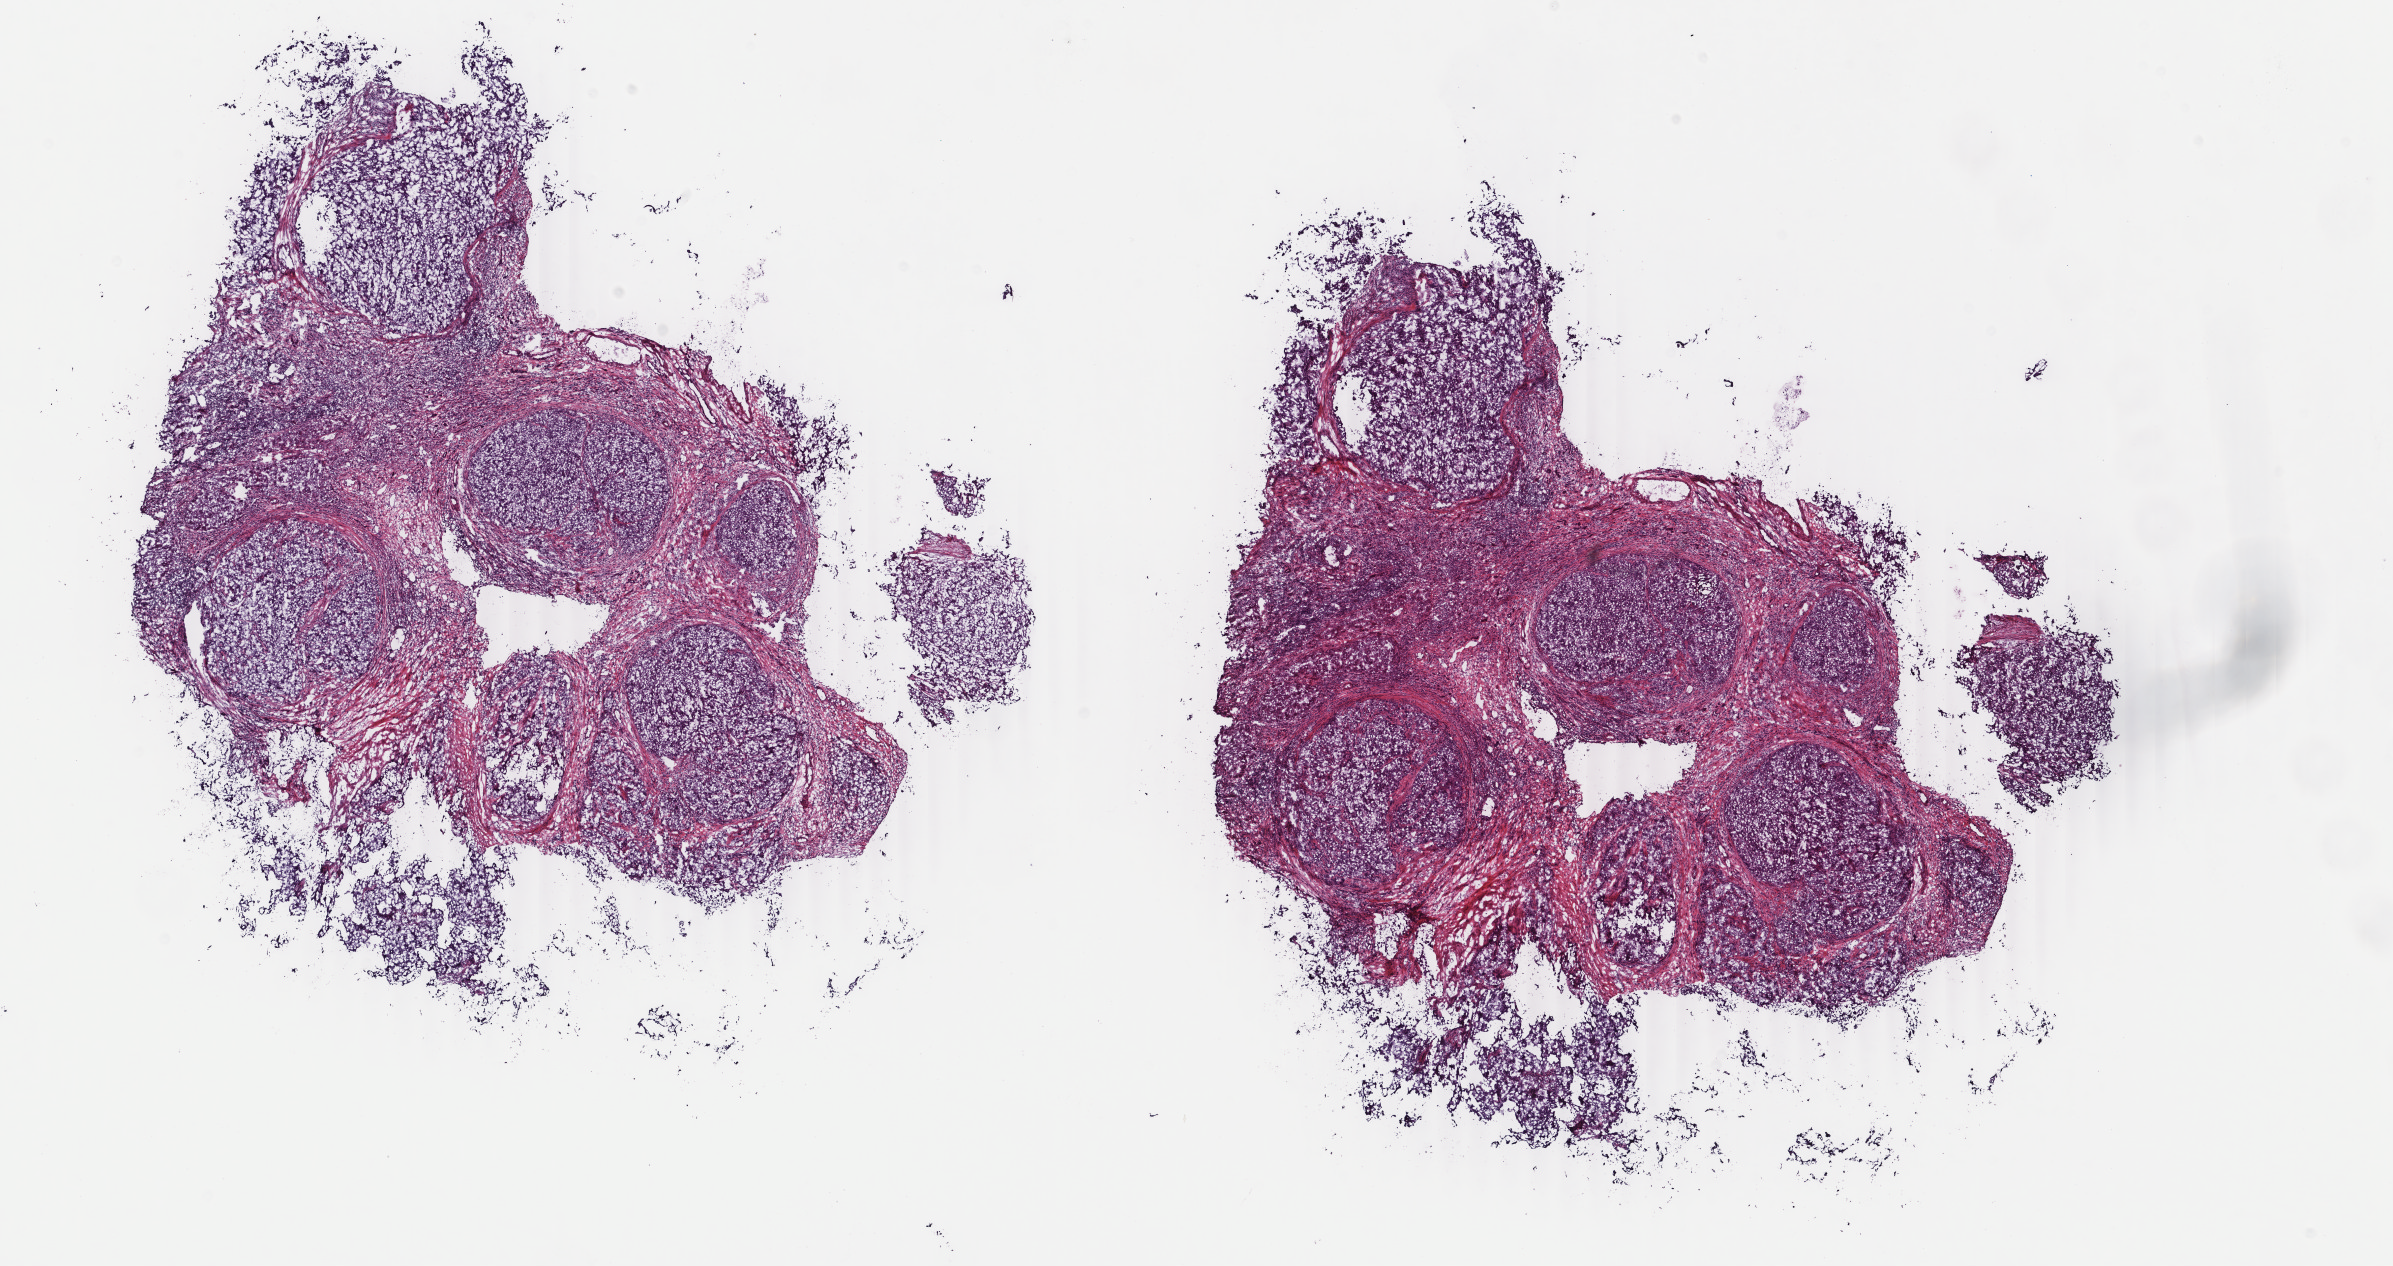
H&E-stained whole-slide image, low-resolution overview of the scanned area, about 19.0 x 10.1 mm (slide scanned at 40x); frozen section from the bottom of the tissue portion; sample: primary tumour, liver. Male, age 42 years at initial diagnosis. Histologic grade: G3 (poorly differentiated). Slide review estimates, as recorded: tumour cells 75%, tumour nuclei 75%, normal cells 2%, stromal cells 23%, necrosis 0%. Inflammatory infiltration, as recorded: lymphocyte infiltration 2%, monocyte infiltration 1%, neutrophil infiltration 2%.
• histologic diagnosis: Hepatocellular carcinoma, NOS
• AJCC pathologic stage: II